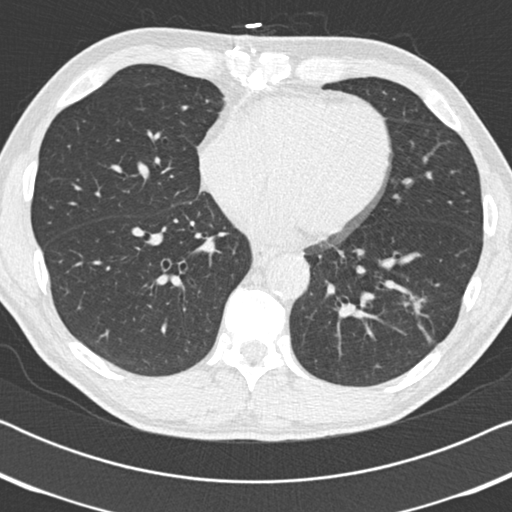
Low-dose screening chest CT, one axial slice; position 73 of 186 along the scan axis; reconstruction kernel B30f; 120 kVp; lung window (W 1500 / L -600 HU); 512 × 512 image matrix.
Annotated regions visible in this slice (outlined manually by an expert reader):
- lesion 1 (tumor, lower lobe of left lung): bounding box (x1, y1, x2, y2) in pixels: (412, 298, 423, 309)